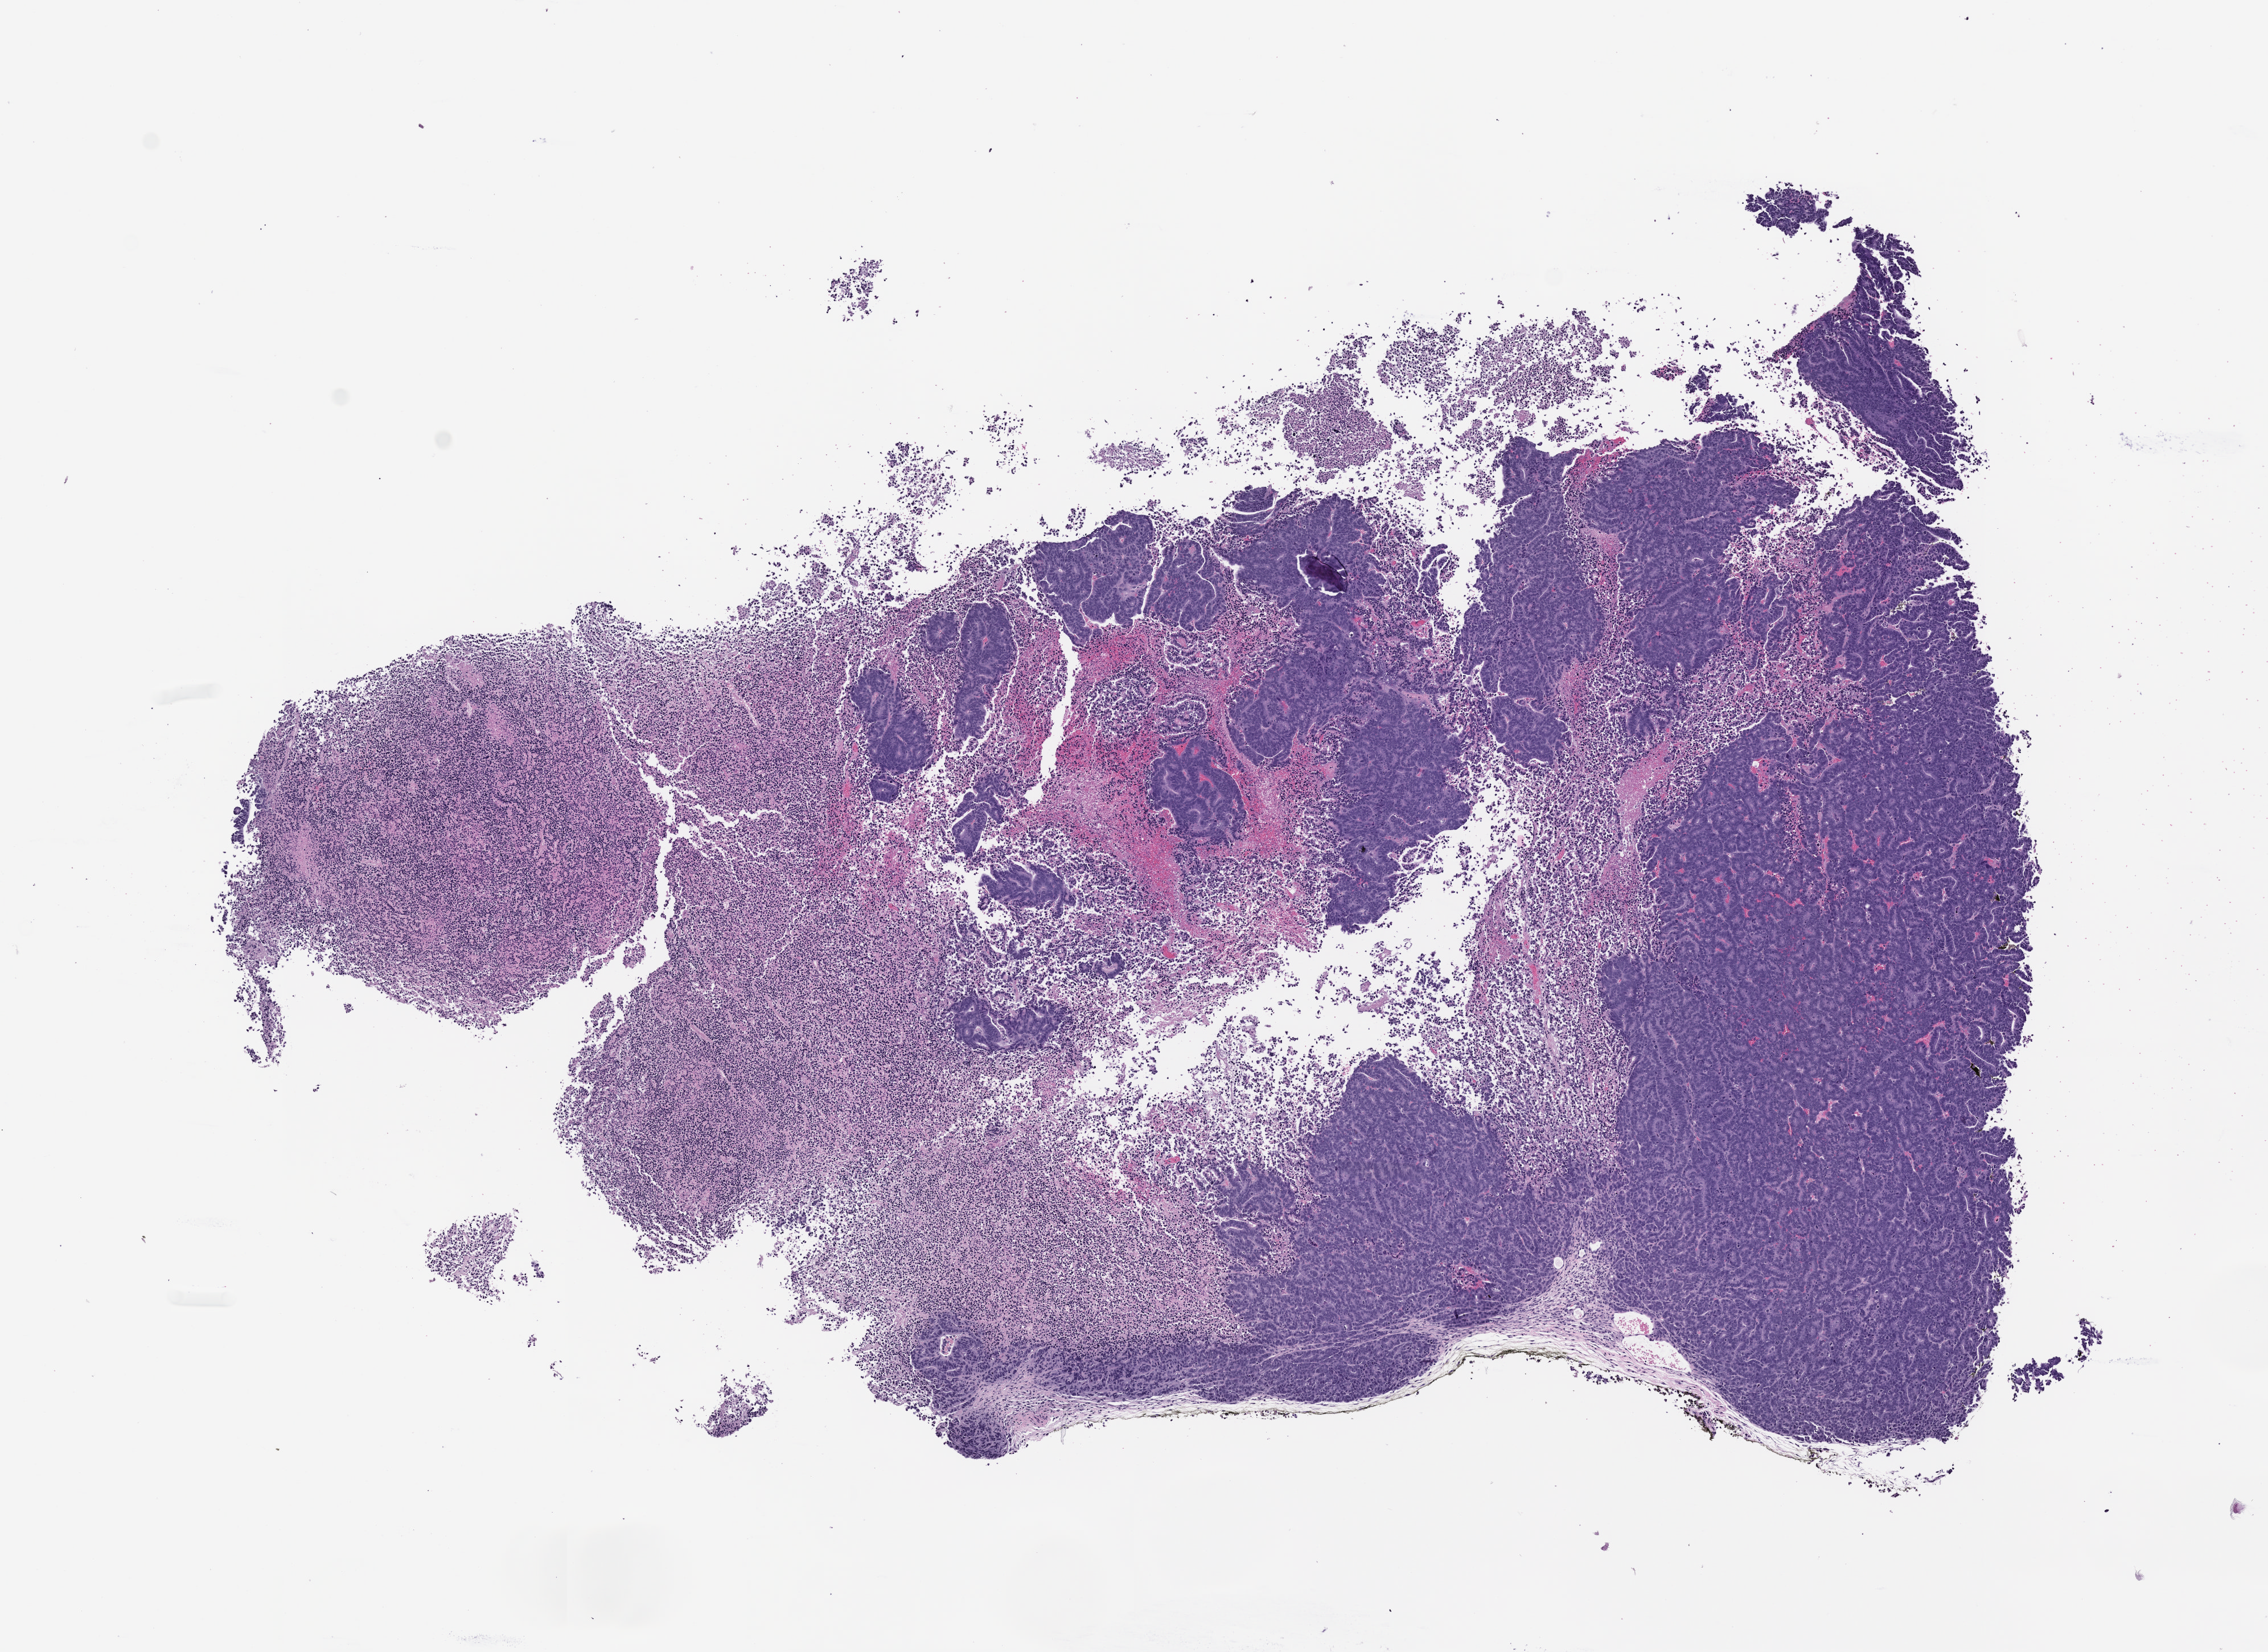
Hematoxylin and eosin (H&E) whole-slide image of a patient-derived xenograft (PDX) tumor grown in a mouse, shown as a low-resolution overview of the whole scanned area (about 8.0 x 5.8 mm), formalin-fixed, paraffin-embedded (FFPE) tissue, originating tumor site category: small intestine.
Originating patient diagnosis: Small Intestinal Adenocarcinoma.